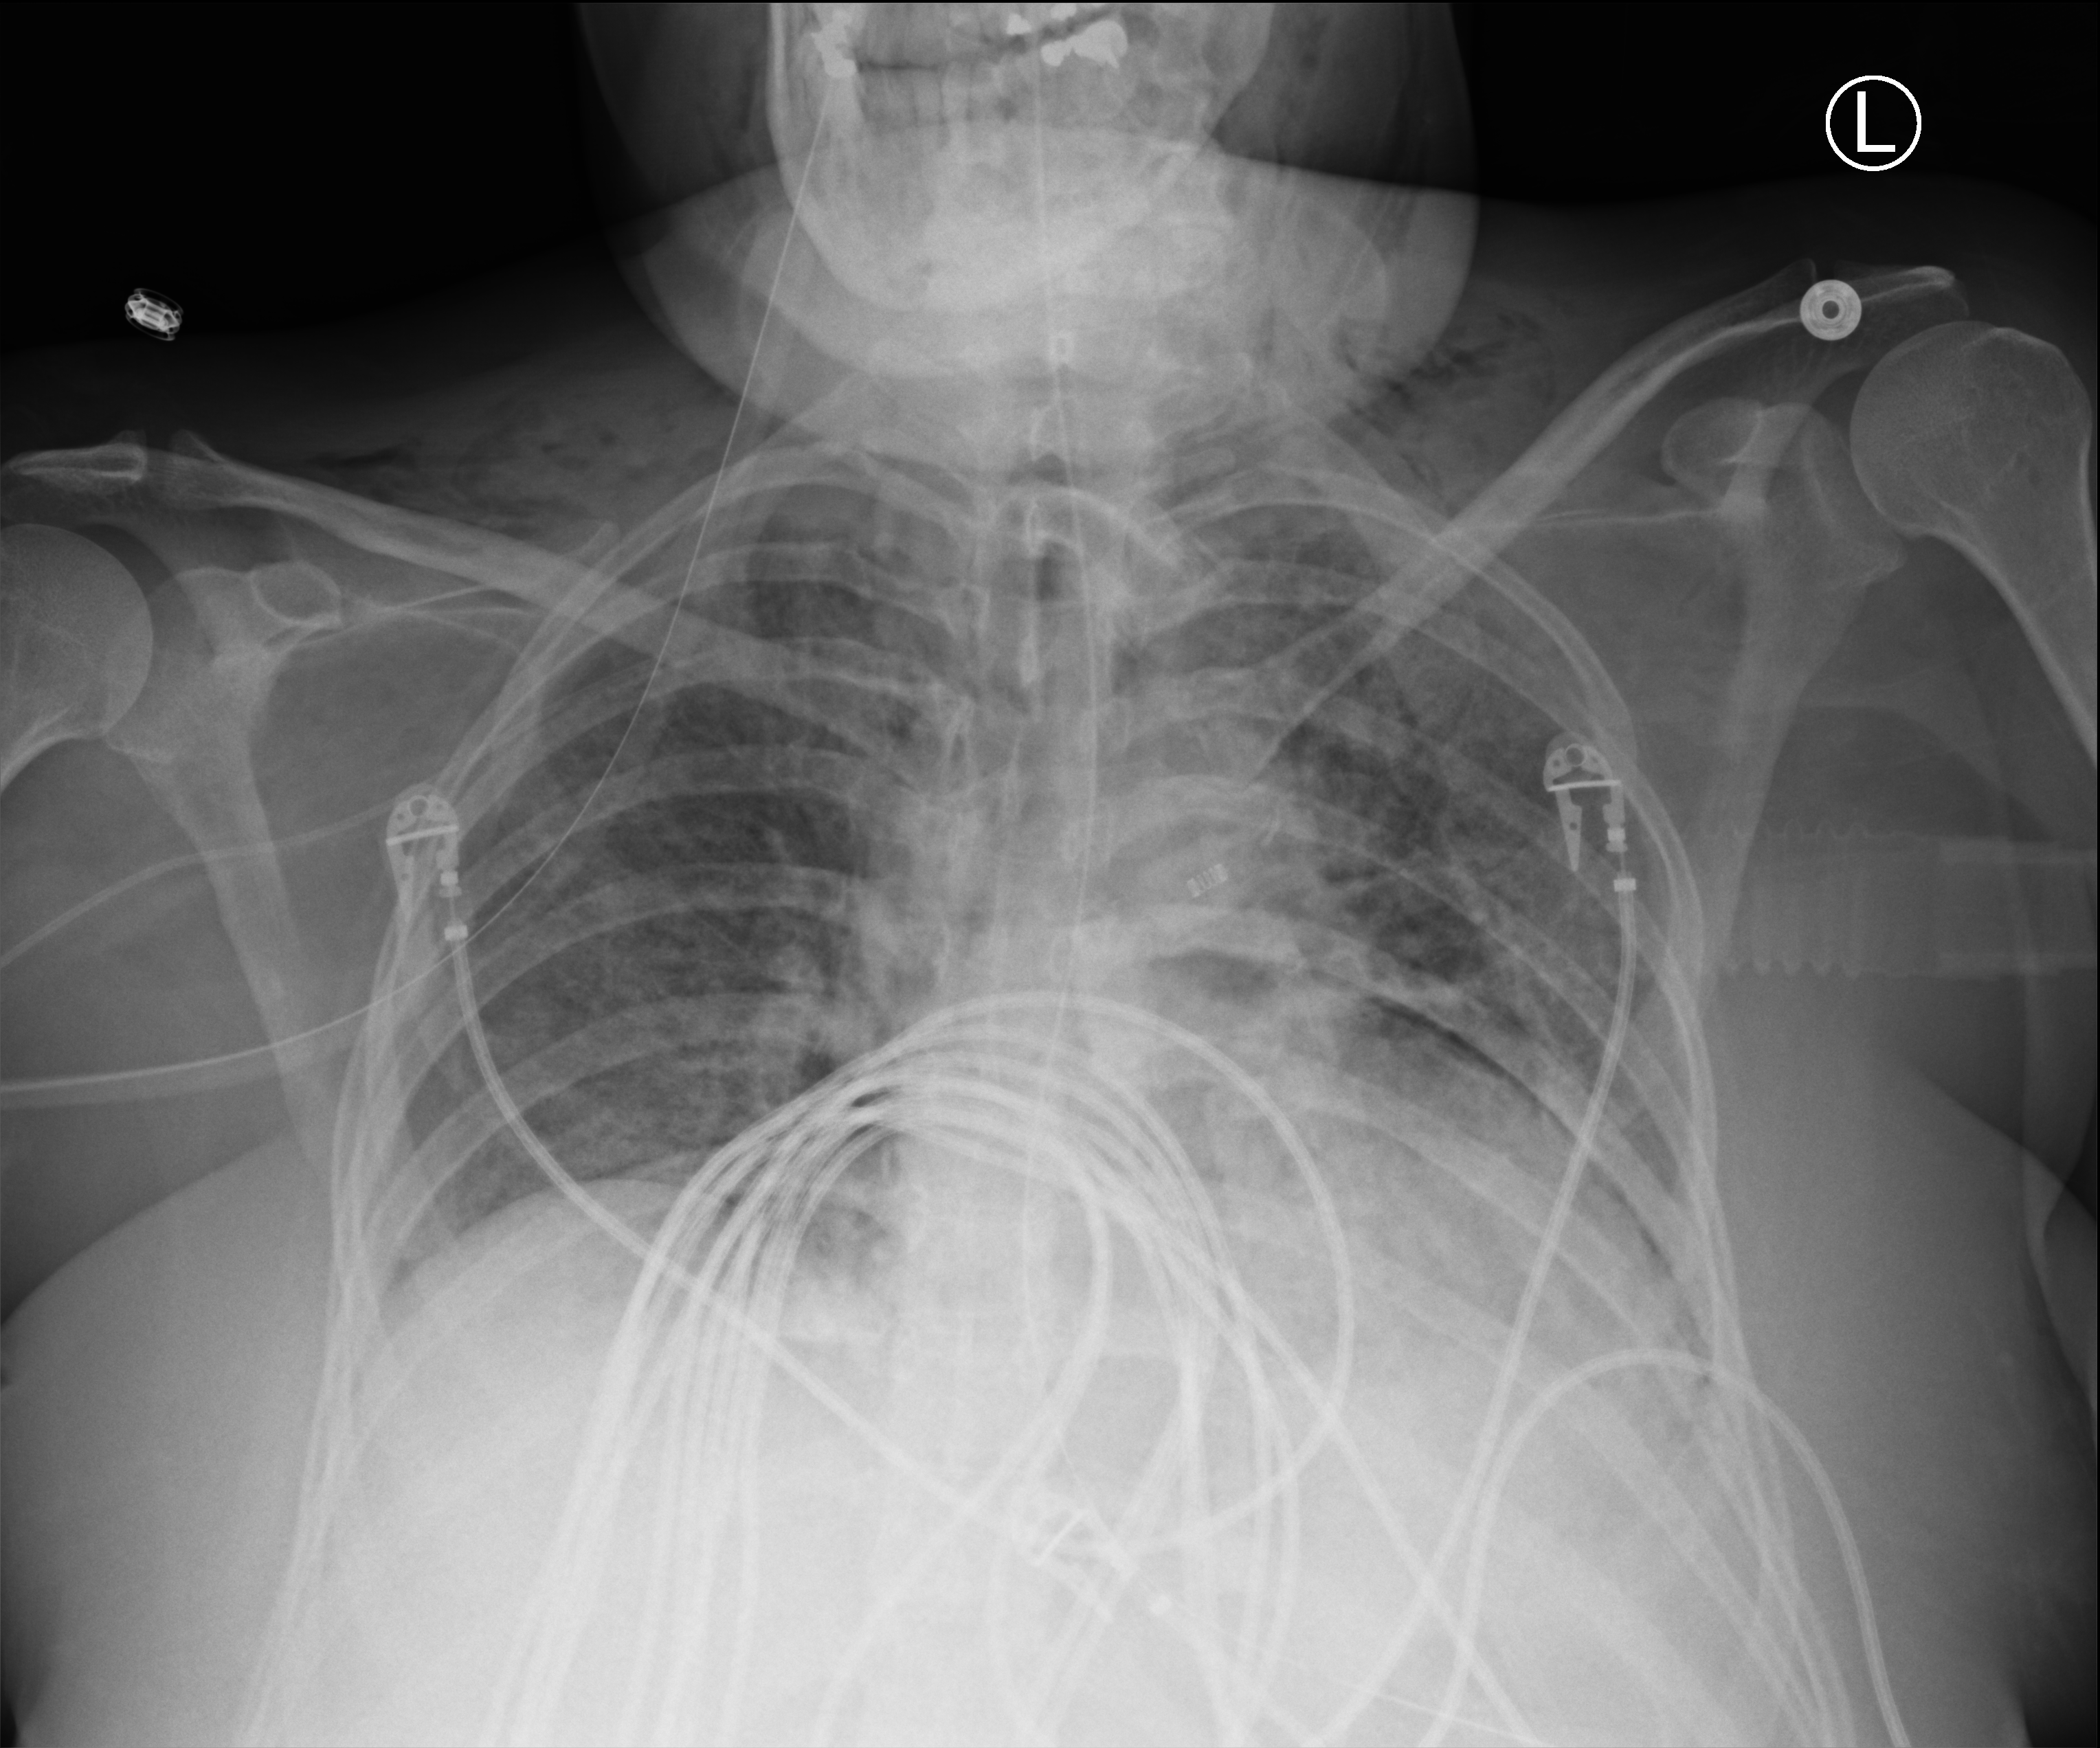
Portable chest radiograph; anteroposterior (AP) projection. Female patient hospitalised with COVID-19, age 18–59 years.
Admission-level facts for this patient (not findings on this image; timing relative to this image not recorded):
- mechanically ventilated during this hospital stay: yes
- COPD (admission record): no
- diabetes (admission record): no